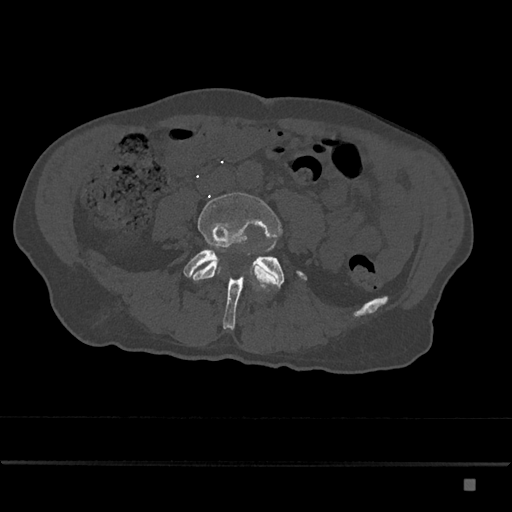
CT including the spine, one axial slice; position 309 of 797 along the scan axis; reconstruction kernel Br40s/3; bone window (W 1800 / L 400 HU); 0.5 mm slice thickness; 512 × 512 image matrix, field of view 390 × 390 mm. Male patient, age 72 years. From the clinical record (not read from this slice): primary cancer: prostate.
Annotated regions visible in this slice (semi-automatically segmented with operator editing):
- L4 vertebra: box from (x=189, y=192) to (x=282, y=287) px
- L5 vertebra: (x=183, y=249)–(x=307, y=330)